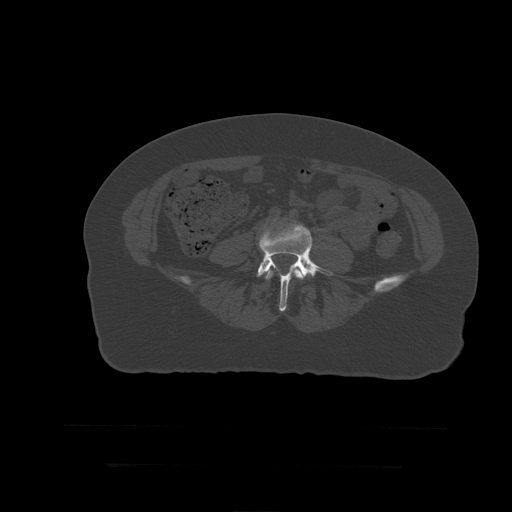
CT including the spine, one axial slice; slice 80 of 399 in the series (ordered by position); 120 kVp; bone window (W 1800 / L 400 HU); 1.25 mm slice thickness; 512 × 512 image matrix, field of view 450 × 450 mm. Patient age 41 years. Case-level facts recorded for this patient, not image findings: primary cancer: breast.
Annotated regions visible in this slice (semi-automatically segmented with operator editing):
- L4 vertebra: bounding box [x1, y1, x2, y2] px = [265, 262, 303, 281]
- L5 vertebra: [257, 225, 333, 312]